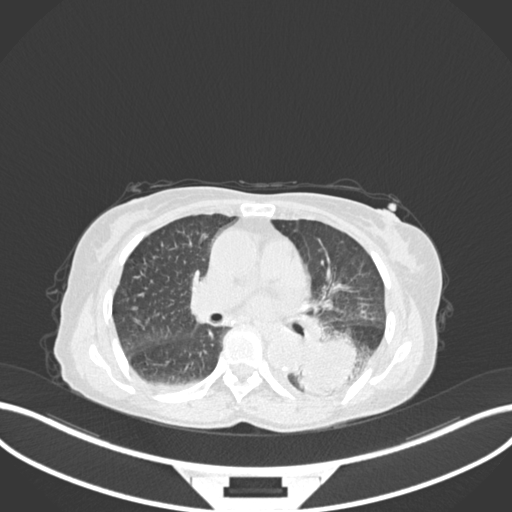
Chest CT, one axial slice. Slice 93 of 233 in the series (ordered by position). 120 kVp. Lung window (W 1500 / L -600 HU). 512 × 512 image matrix, field of view 400 × 400 mm. Female patient, age 78 years. Case-level facts recorded for this patient, not image findings: clinical TNM (as recorded): T3 N0 M1.
Annotated regions visible in this slice (bounding box drawn by a radiologist):
- lung tumour (recorded histology: squamous cell carcinoma): box from (x=299, y=325) to (x=370, y=392) px